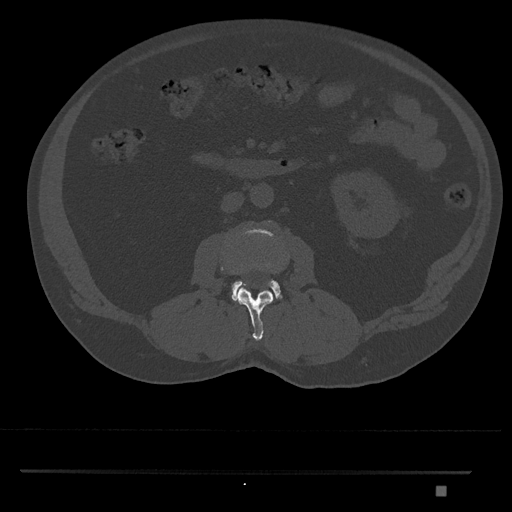
CT including the spine, one axial slice. Slice 722 of 1134 in the series (ordered by position). 120 kVp. Bone window (W 1800 / L 400 HU). 0.5 mm slice thickness. 512 × 512 image matrix, field of view 429 × 429 mm. Male patient, age 65 years. Case-level facts recorded for this patient, not image findings: primary cancer: prostate.
Annotated regions visible in this slice (semi-automatically segmented with operator editing):
- L2 vertebra: bounding box [x1, y1, x2, y2] px = [221, 267, 273, 341]
- L3 vertebra: [232, 229, 282, 303]